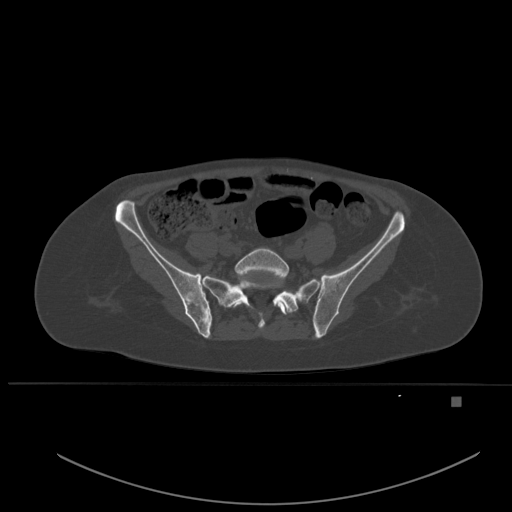
CT including the spine, one axial slice. Slice 144 of 651 in the series (ordered by position). Bone window (W 1800 / L 400 HU). 1.5 mm slice thickness. 512 × 512 image matrix. Patient: female, 49 years. Case-level facts recorded for this patient, not image findings: primary cancer: breast; vertebrae with lytic lesions (as recorded): L3, T12, L4.
Outlined on this slice (semi-automatically segmented with operator editing):
- L5 vertebra: bounding box (x1, y1, x2, y2) in pixels: (233, 248, 292, 315)